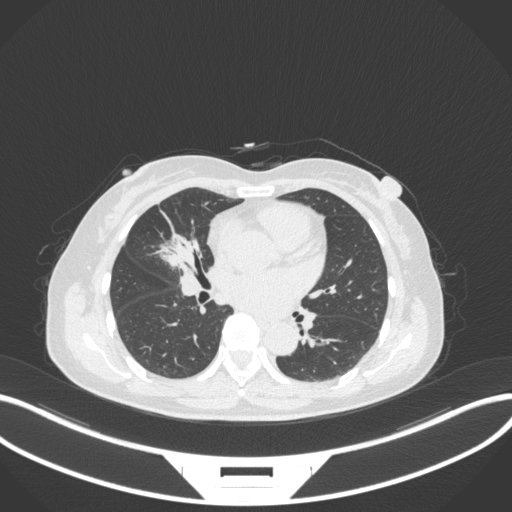
Chest CT, one axial slice; reconstruction kernel B31f; lung window (W 1500 / L -600 HU); 512 × 512 image matrix, field of view 400 × 400 mm. Female patient, age 51 years. Case-level facts recorded for this patient, not image findings: clinical TNM (as recorded): T1c N0 M0; histopathological grade: G2.
Outlined on this slice (bounding box drawn by a radiologist):
- lung tumour (recorded histology: adenocarcinoma): box from (x=151, y=230) to (x=201, y=273) px